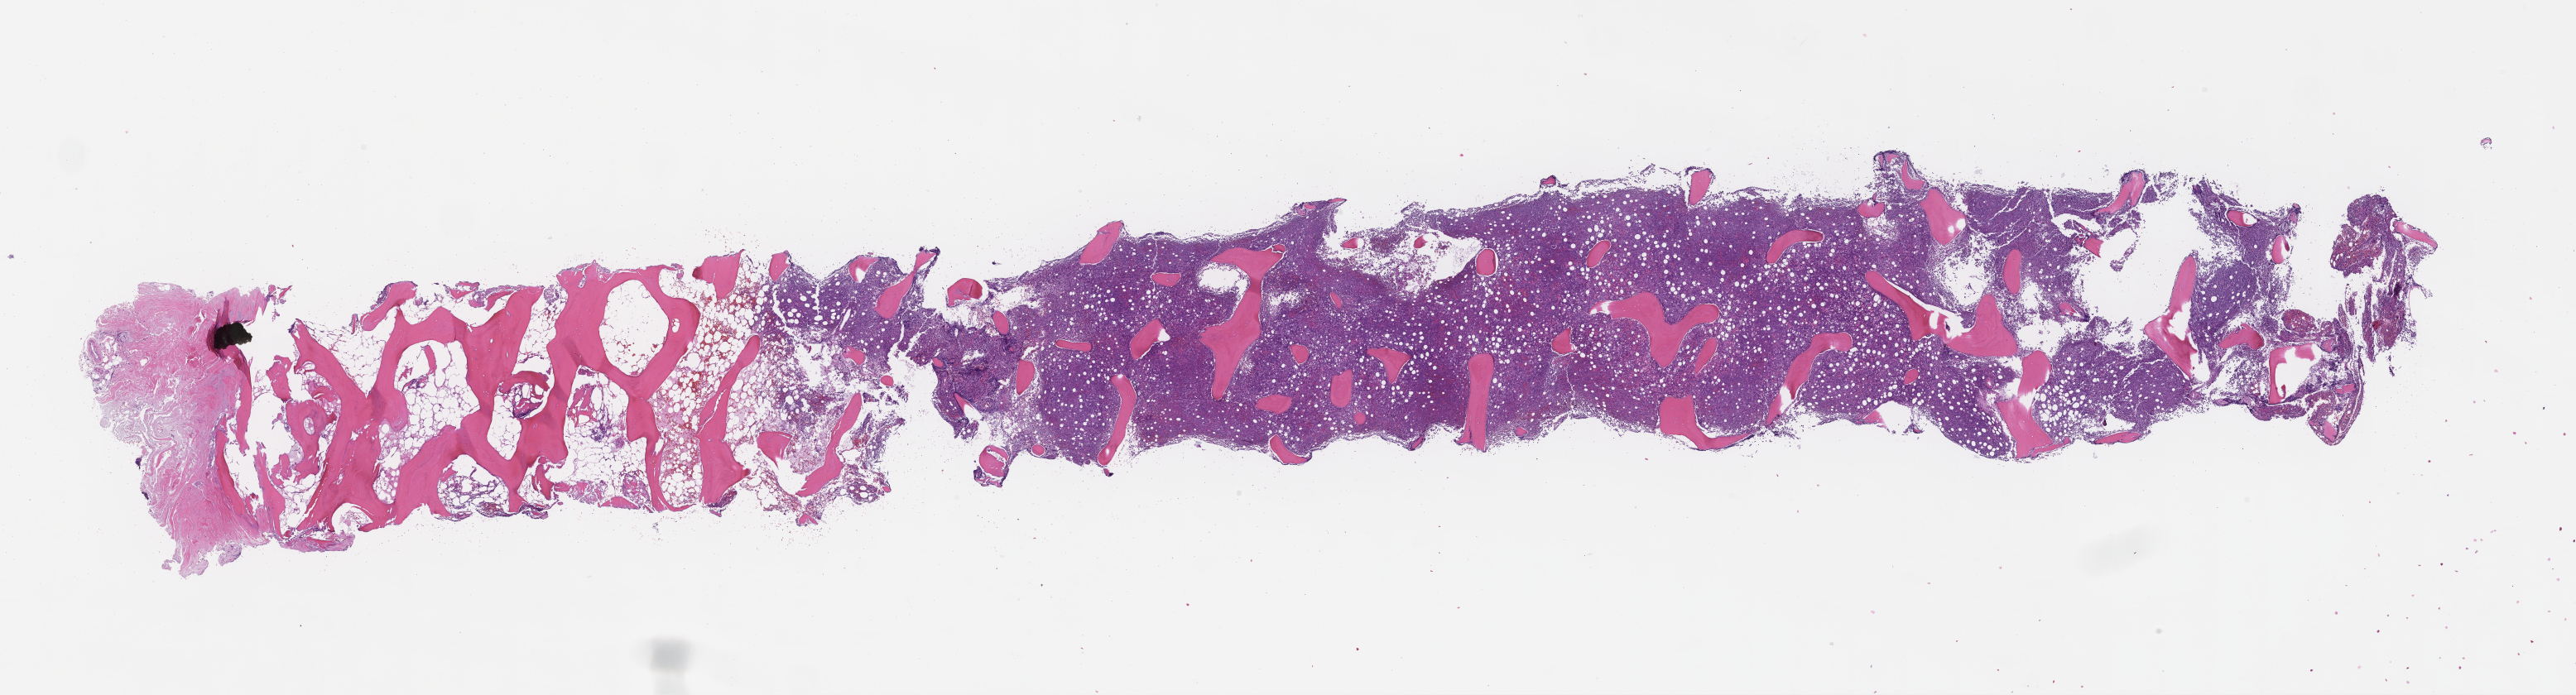
Whole-slide image, hematoxylin and eosin (H&E) stain — a low-resolution overview of the entire scanned area, about 25.1 x 6.8 mm, formalin-fixed paraffin-embedded section, site: bone marrow. Patient sex: male.
This section: primary tumor. Diagnosis: Acute Myeloid Leukemia Not Otherwise Specified.